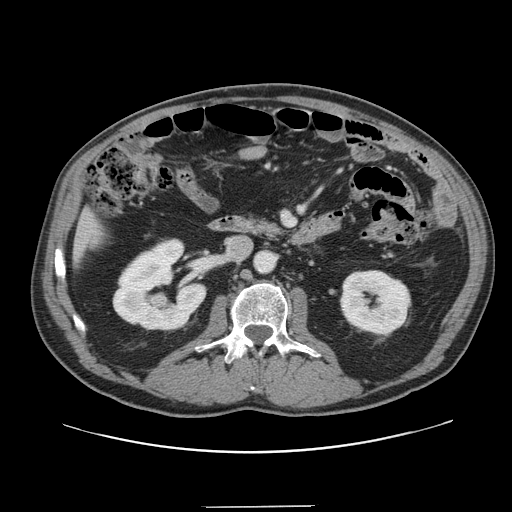
Contrast-enhanced abdominal CT, one axial slice. Position 53 of 139 along the scan axis. Intravenous contrast given. Soft-tissue window (W 400 / L 40 HU). 2.5 mm slice thickness. 512 × 512 image matrix, field of view 397 × 397 mm. Male patient, age 64 years. Case-level facts recorded for this patient, not image findings: diagnosis: colorectal cancer liver metastases, imaged before liver resection; multiple liver metastases: yes.
Annotated regions visible in this slice (outlined manually by an expert reader):
- liver: bounding box (x1, y1, x2, y2) in pixels: (76, 214, 100, 261)
- planned liver remnant (the part of the liver to remain after resection): (76, 215, 99, 262)